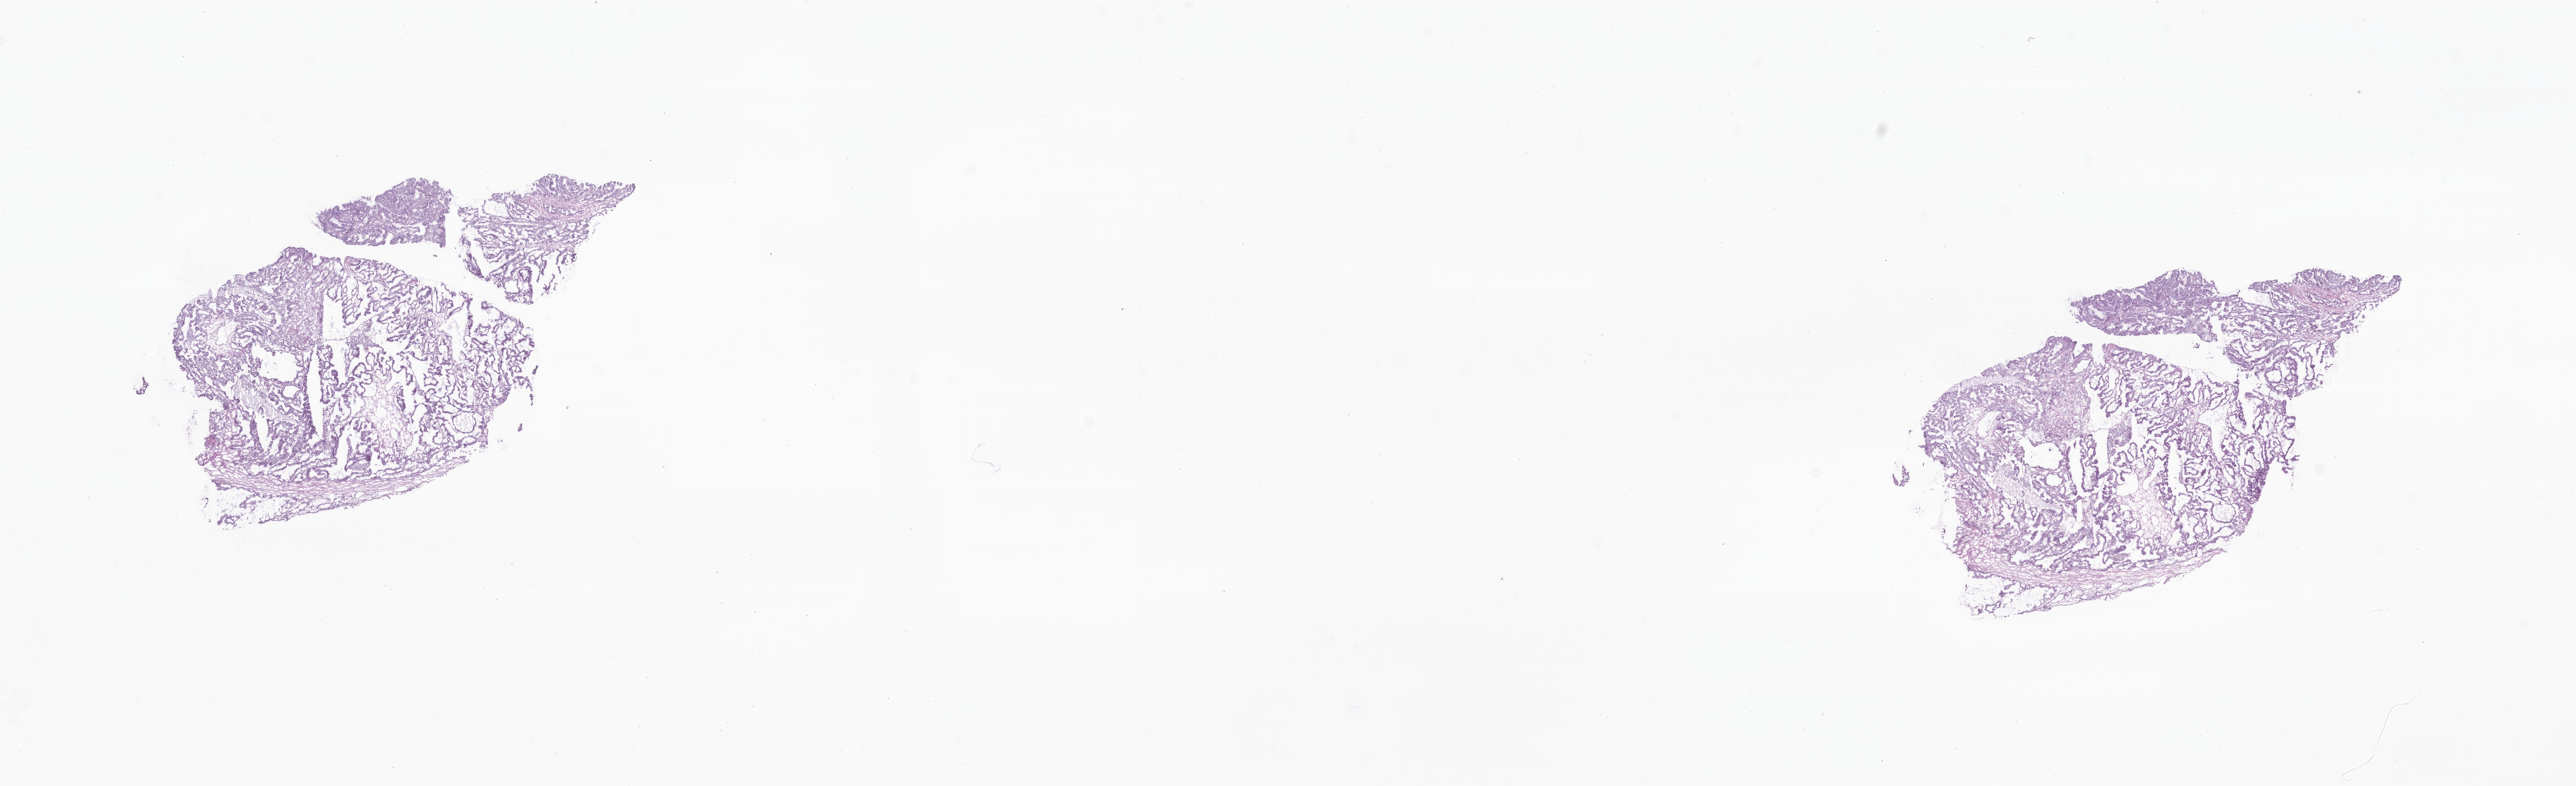
Whole-slide image, haematoxylin and eosin stain of tumor tissue from the brain — shown as a low-resolution overview of the whole scanned area (about 27.4 x 8.4 mm); cryosection (OCT / tissue freezing medium). Patient female; age 69 days.
Diagnosis: Choroid plexus carcinoma.